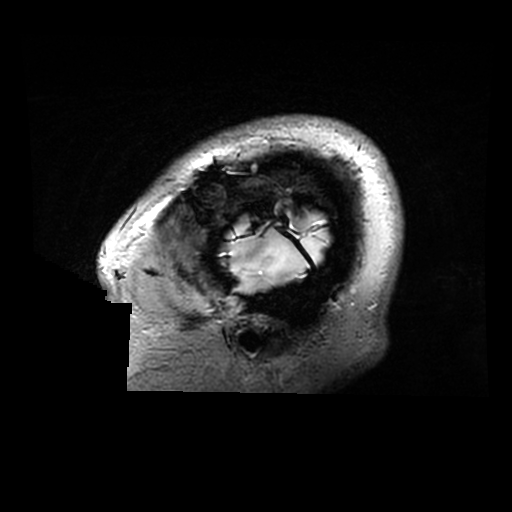
Brain MRI from a brain-tumour surgery series, one sagittal slice; position 259 of 320 along the scan axis; 0.6 mm slice thickness; 512 × 512 image matrix, field of view 240 × 240 mm. Case-level facts recorded for this patient, not image findings: histopathology: Astrocytoma; WHO grade: 2; IDH mutation: yes.
Structures marked on this image (expert manual segmentation):
- tumour: box from (x=221, y=217) to (x=330, y=283) px